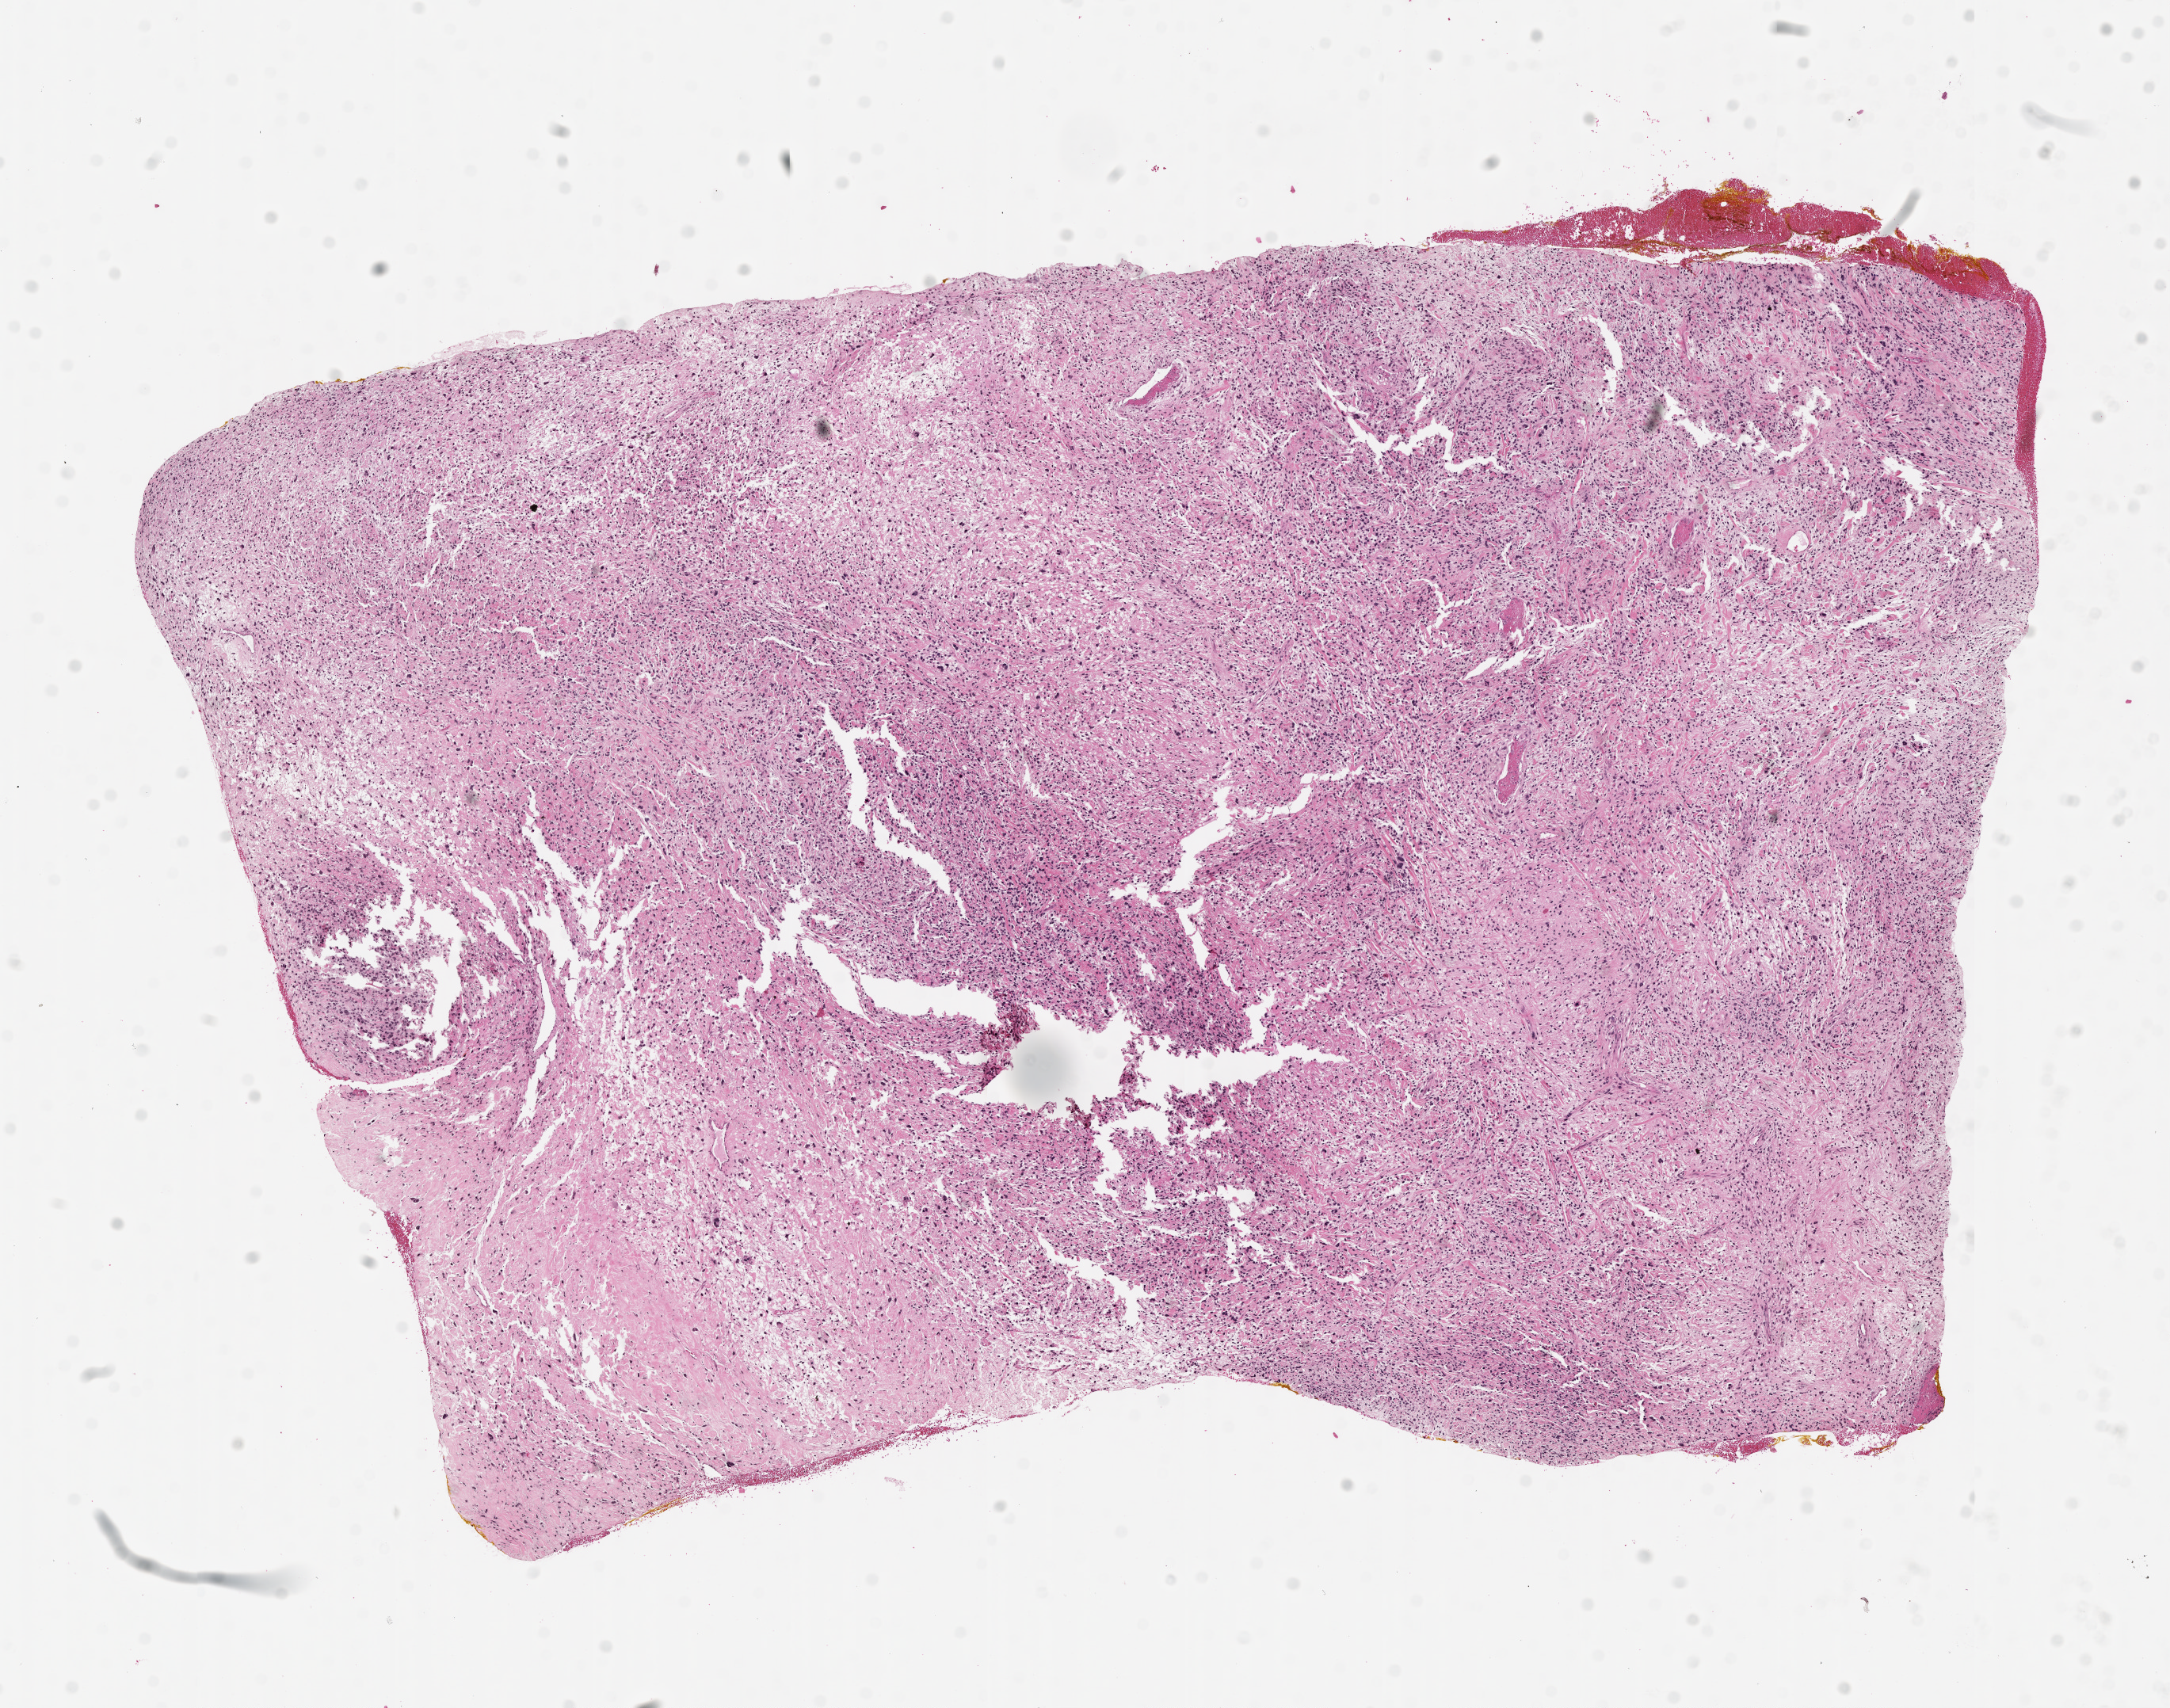
Whole-slide histology image, H&E-stained — low-resolution overview of the scanned area, about 11.0 x 8.7 mm (slide scanned at 20x).
* patient diagnosis (cohort enrolment): sarcoma (site not recorded at cohort level)